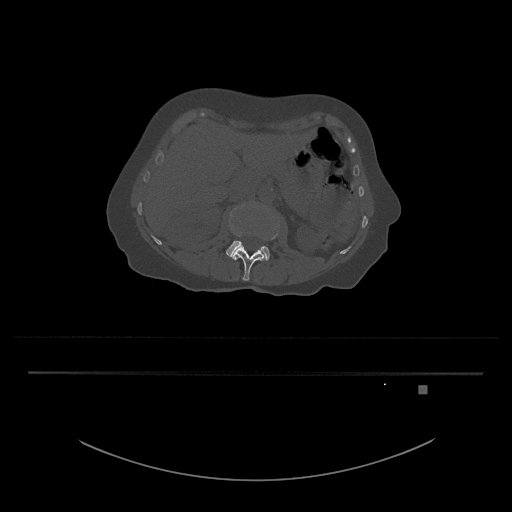
CT including the spine, one axial slice; slice 467 of 797 in the series (ordered by position); bone window (W 1800 / L 400 HU); 0.5 mm slice thickness; 512 × 512 image matrix. Patient: female, 57 years. Case-level facts recorded for this patient, not image findings: primary cancer: cervical.
Annotated regions visible in this slice (semi-automatically segmented with operator editing):
- L3 vertebra: bounding box [x1, y1, x2, y2] px = [226, 205, 279, 260]